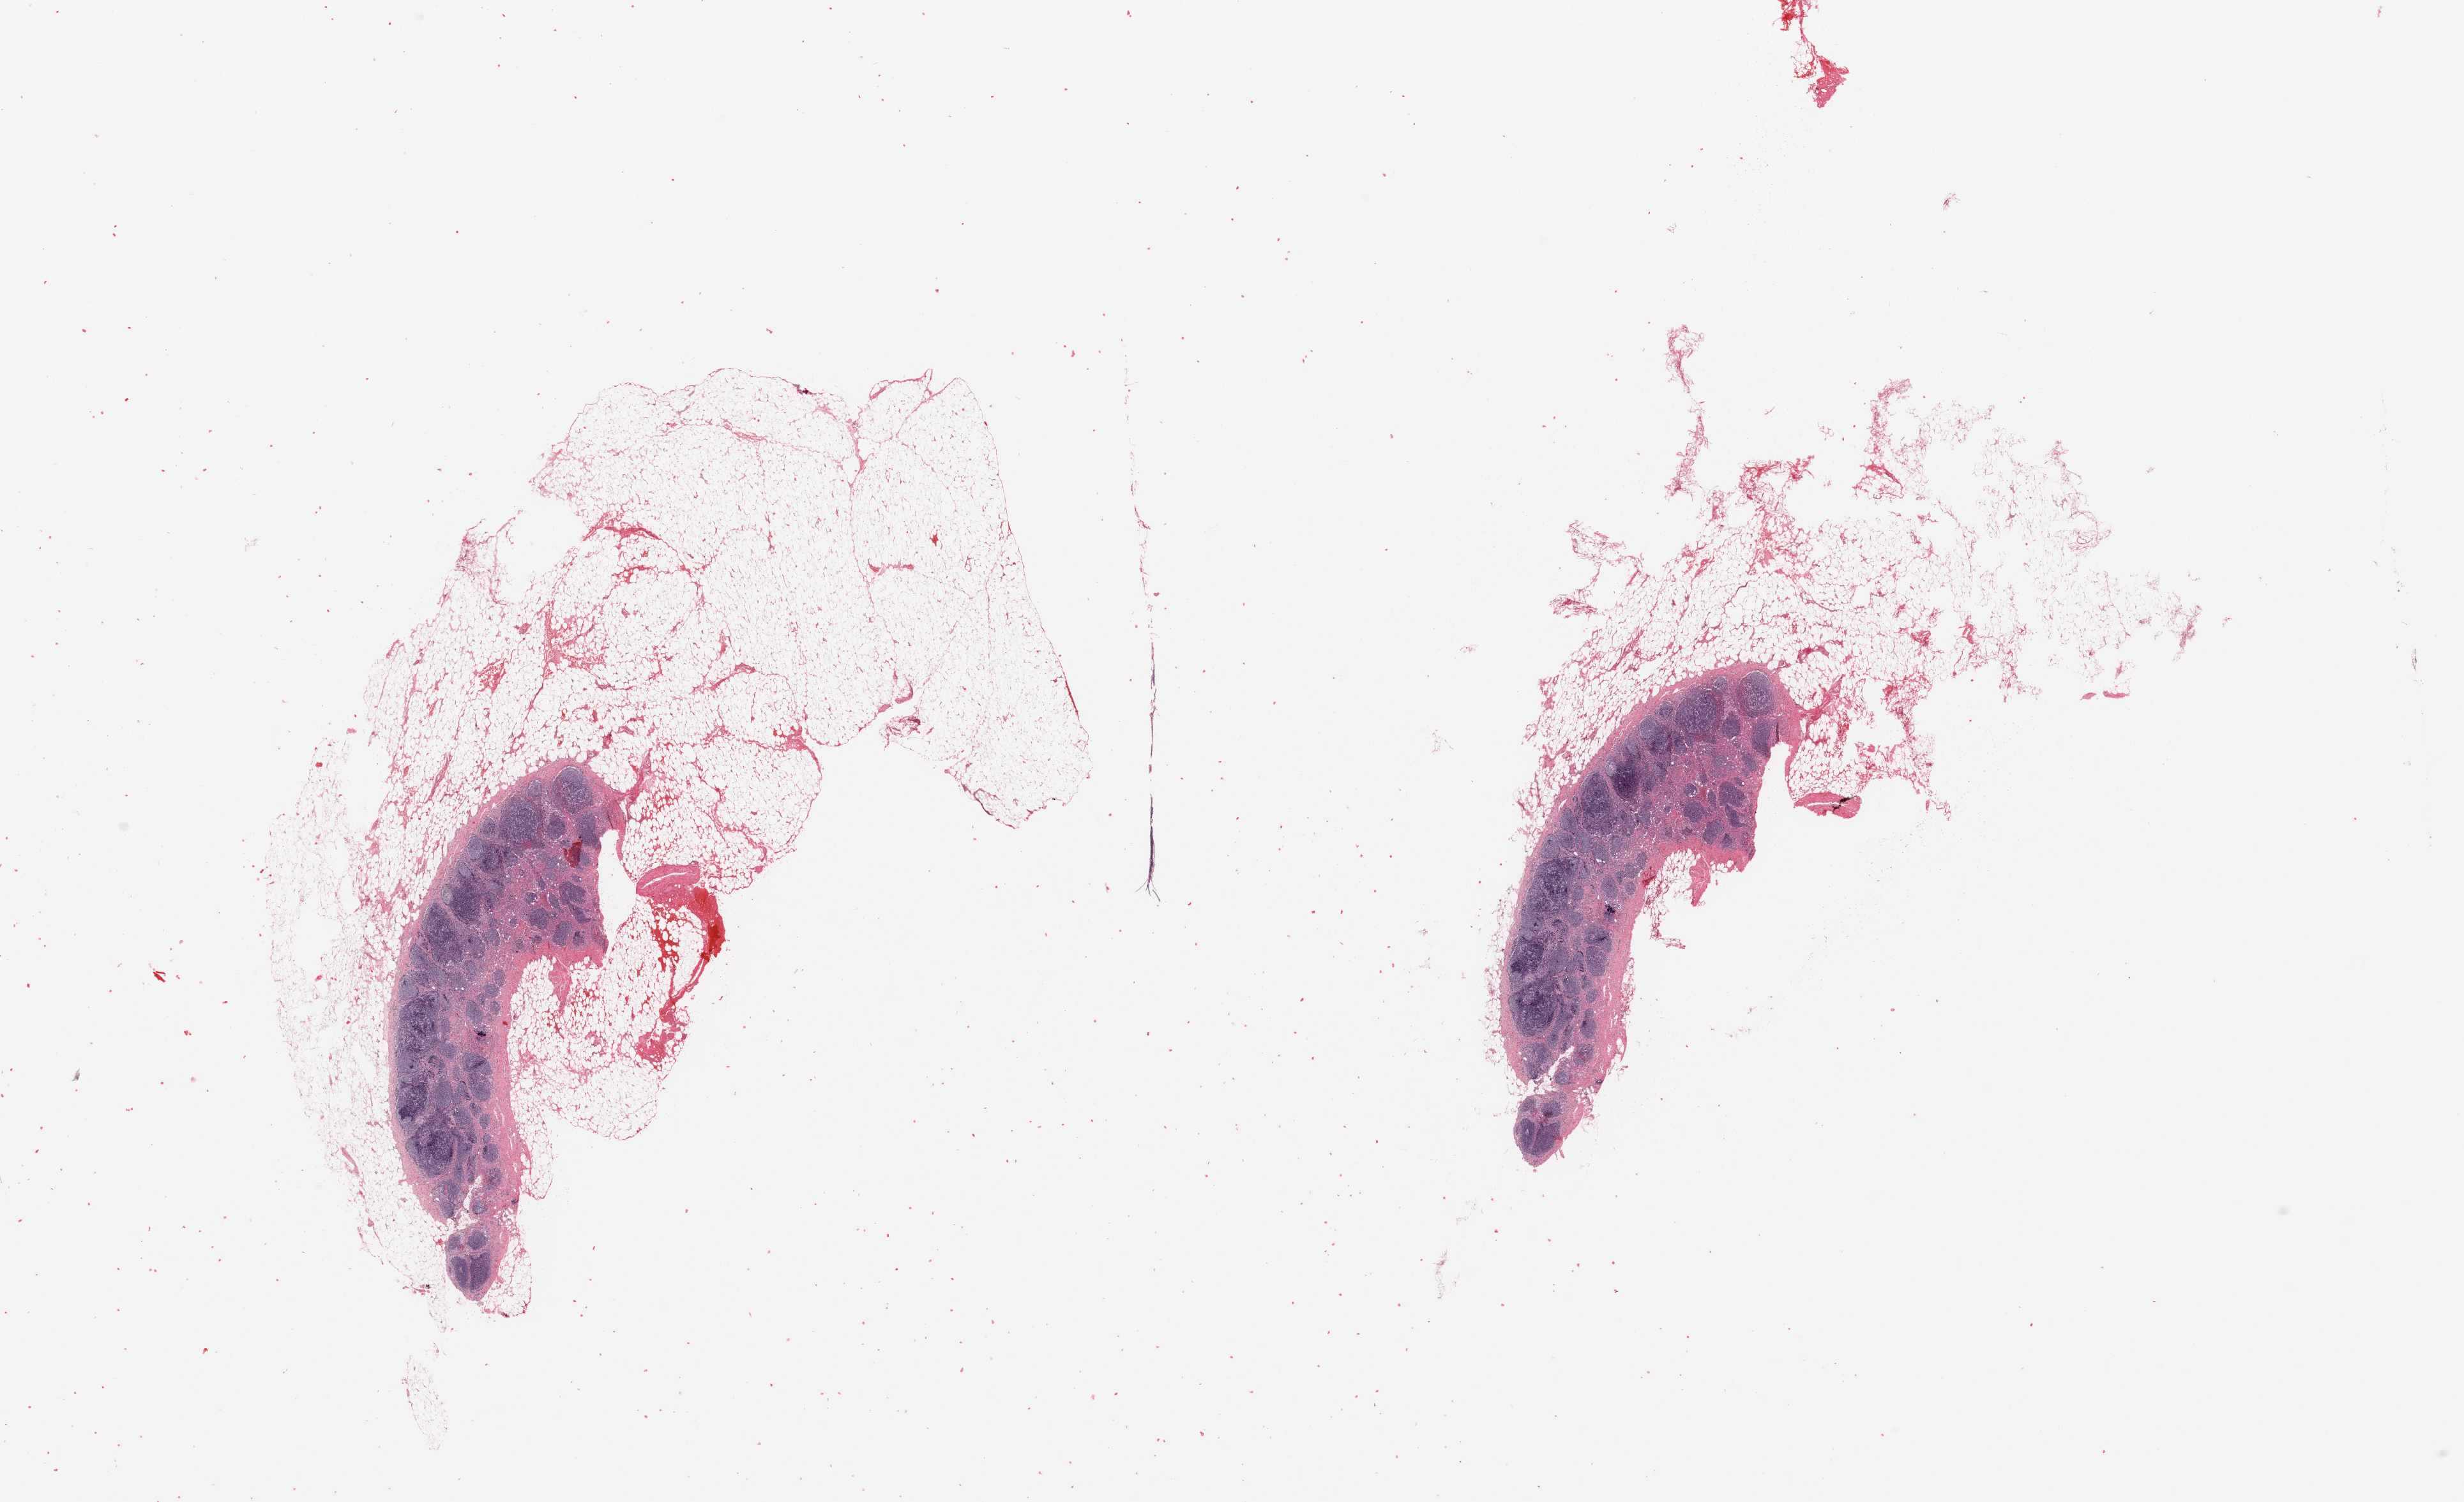
H&E-stained whole-slide image — low-resolution overview of the scanned area, about 30.5 x 18.6 mm (from a 20x scan). Normal (non-tumour) tissue sample, pancreas. Patient: male, age 84 years.
This section: normal (non-tumour) tissue from the same patient. Patient diagnosis (cohort enrolment): ductal adenocarcinoma (pancreas).